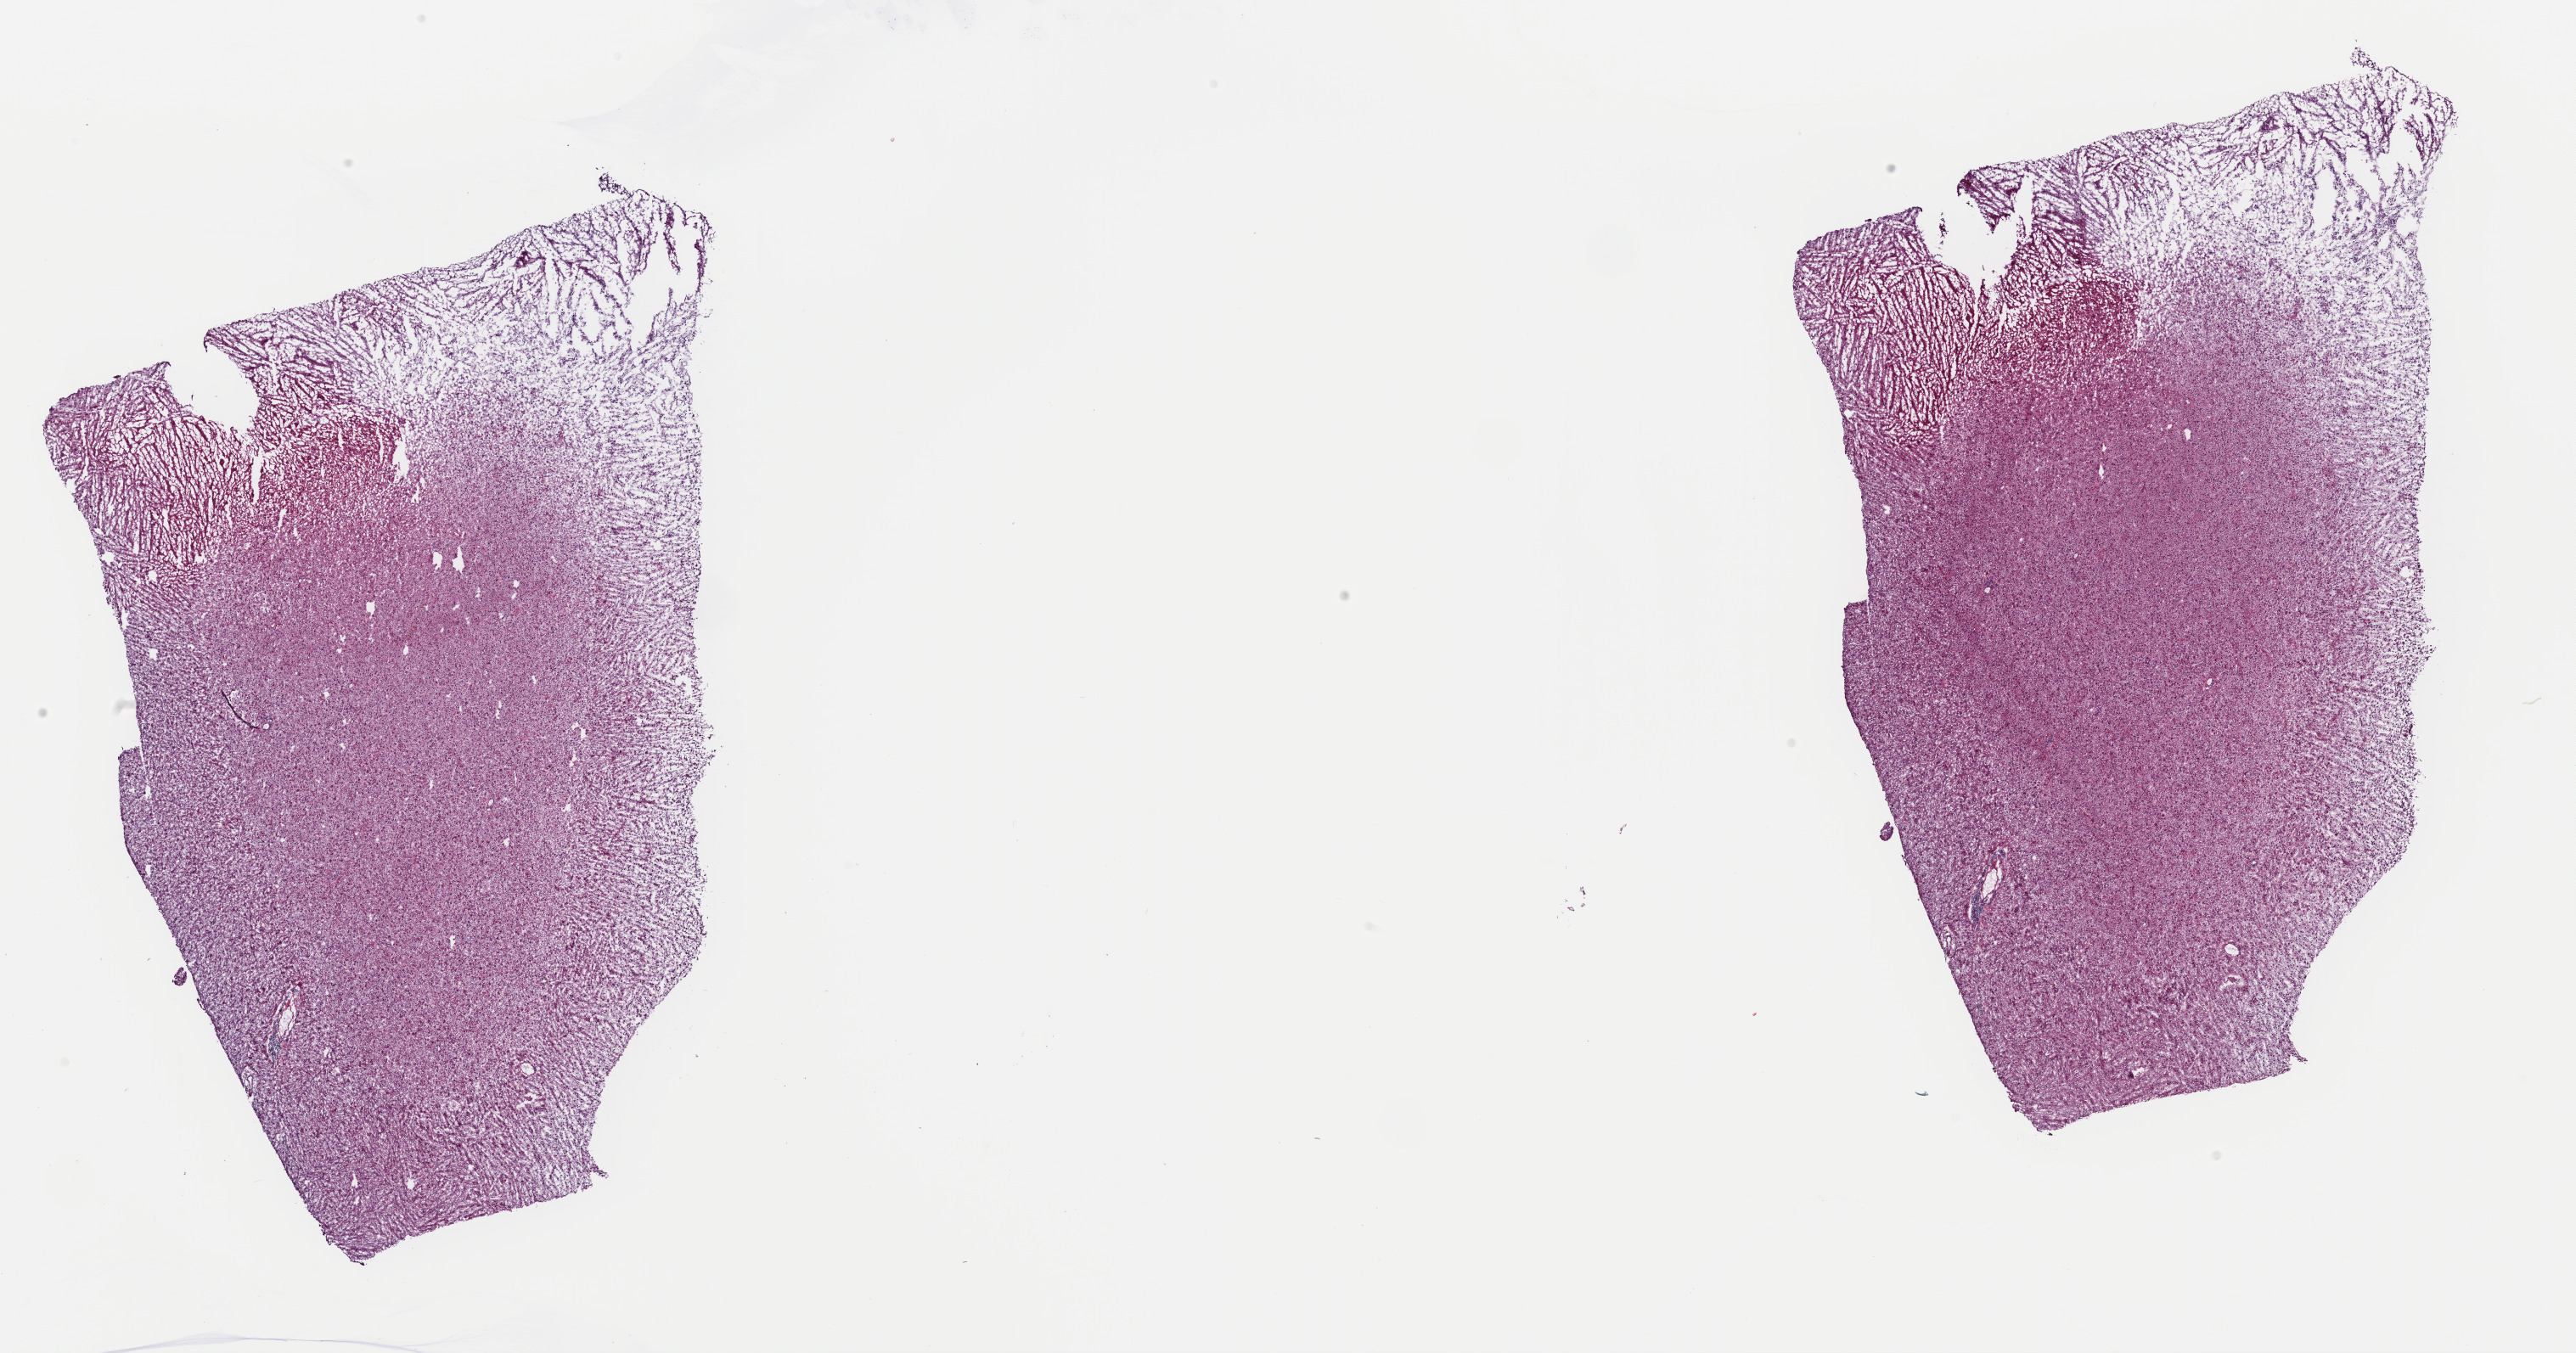
Whole-slide histology image, Hematoxylin and eosin (H&E) stained, shown as a low-resolution overview of the whole scanned area (about 24.0 x 12.6 mm, from a 40x scan); frozen section from the top of the tissue portion; primary tumour sample from the brain. Patient: male, age at initial diagnosis 51 years. Histologic grade: G2 (moderately differentiated). Pathologist review of this section (percent, as recorded): tumour cells 85%, tumour nuclei 90%, normal cells 10%, stromal cells 5%, necrosis 0%. Infiltration values recorded for this section: lymphocyte infiltration 5%, monocyte infiltration 0%, neutrophil infiltration 0%.
Diagnosis: Mixed glioma (cerebrum).